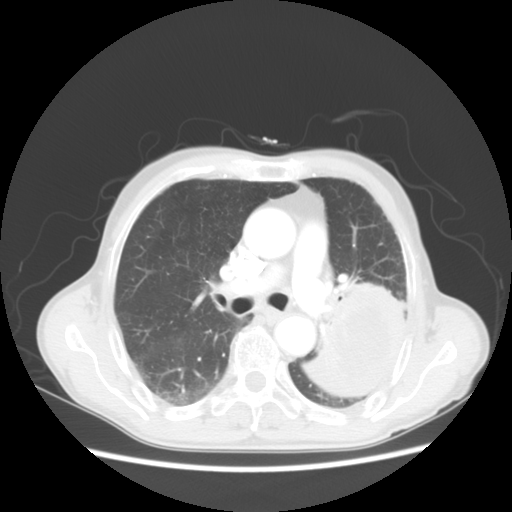
Chest CT, one axial slice; position 32 of 51 along the scan axis; 120 kVp; lung window (W 1500 / L -600 HU); 5 mm slice thickness; 512 × 512 image matrix, field of view 360 × 360 mm. Male patient, age 64 years. From the clinical record (not read from this slice): clinical TNM (as recorded): T4 N0 M0.
Annotated regions visible in this slice (rectangle marked by the reading radiologist):
- lung tumour (recorded histology: squamous cell carcinoma): bounding box [x1, y1, x2, y2] px = [315, 273, 398, 415]